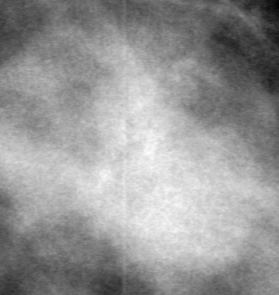
Crop from a digitized film mammogram around one marked abnormality, right breast, MLO view, BI-RADS breast density category 2 (scale 1–4).
- Finding: mass, shape oval, margins circumscribed; BI-RADS assessment category 3; pathology result (as recorded, not read from the image): benign.